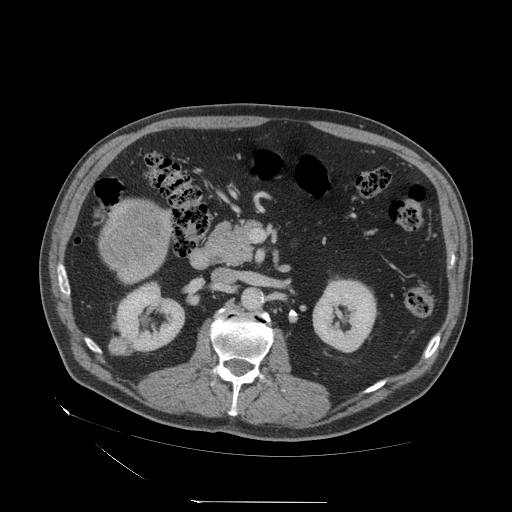
Contrast-enhanced abdominal CT (liver protocol), one axial slice. Slice 8 of 83 in the series (ordered by position). Reconstruction kernel STANDARD. 140 kVp. Soft-tissue window (W 400 / L 40 HU). 512 × 512 image matrix, field of view 460 × 460 mm. From the clinical record (not read from this slice): diagnosis: hepatocellular carcinoma (patient treated with transarterial chemoembolisation; whether this scan precedes or follows treatment is not stated here); TNM stage (as recorded): Stage-I; Child-Pugh class: A; tumour differentiation: well differentiated; tumour nodularity: uninodular.
Structures marked on this image (semi-automatic segmentation, software-assisted and operator-edited):
- mass: bounding box [x1, y1, x2, y2] px = [100, 200, 174, 269]